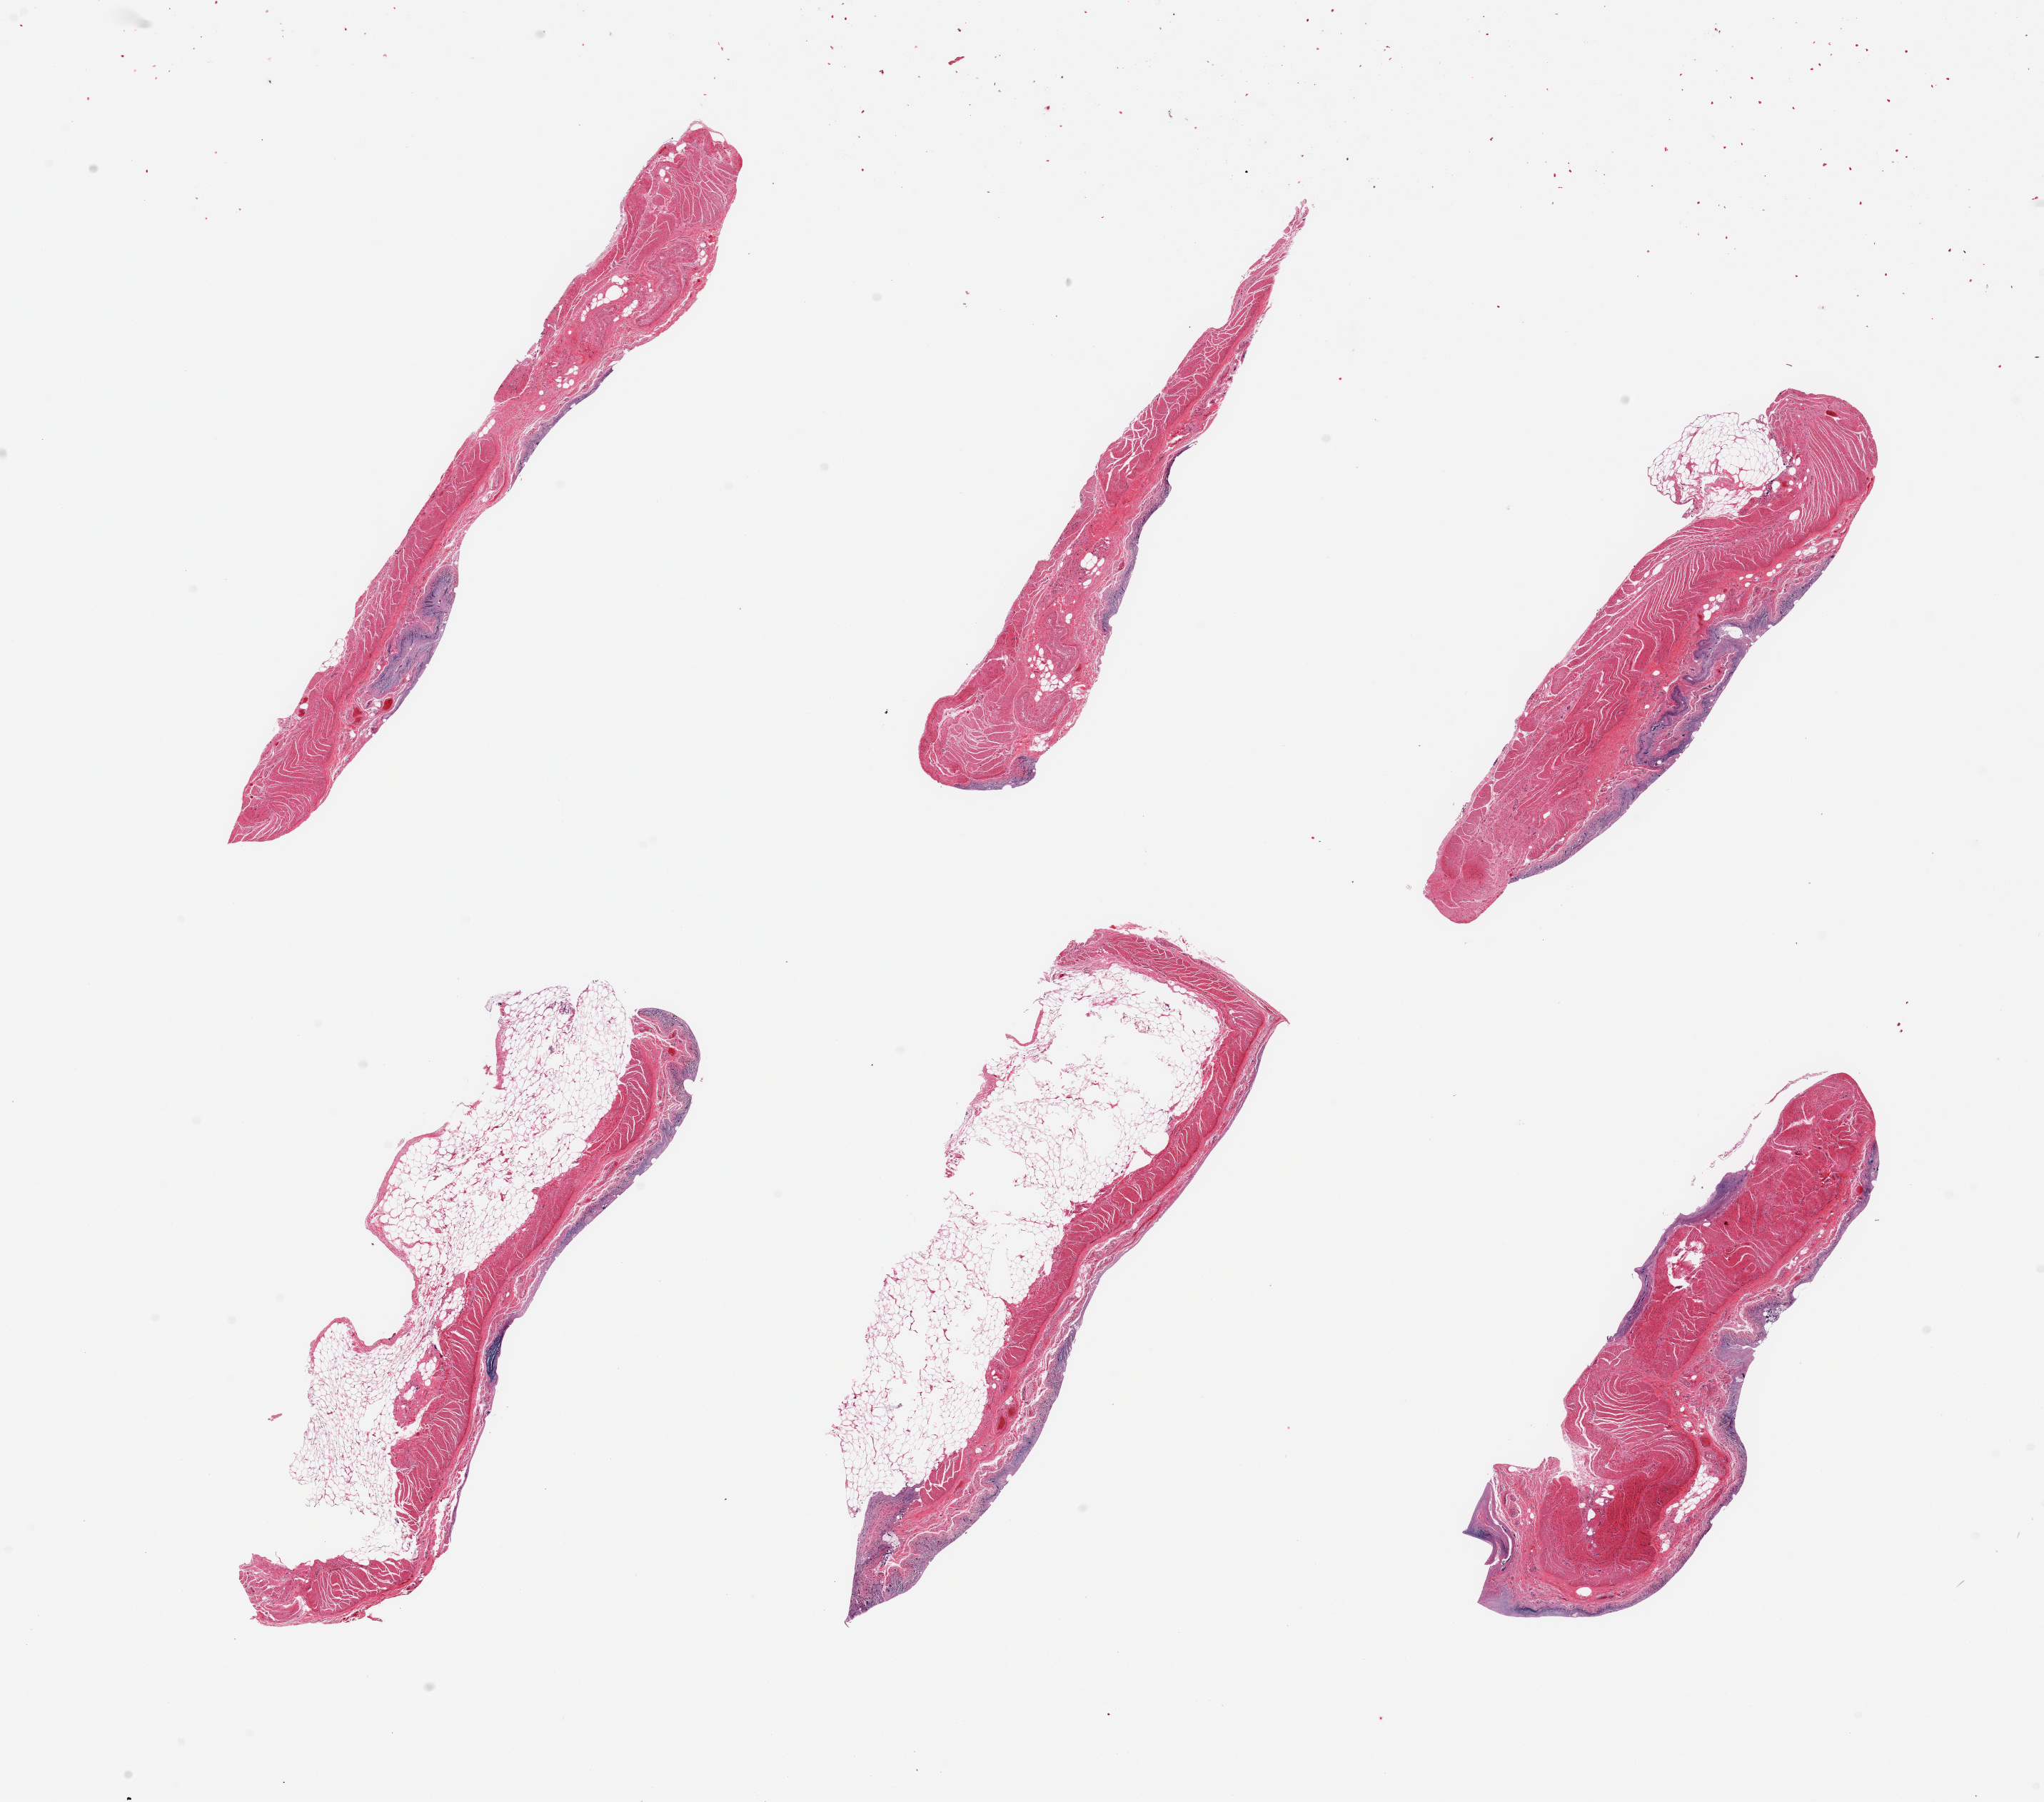
Haematoxylin and eosin whole-slide image — shown as a low-resolution overview of the whole scanned area (about 22.6 x 20.0 mm). PAXgene-fixed, paraffin-embedded tissue. Section of ileum (target tissue). Tissue donor sample.
Pathologist's review note for this sample: 6 pieces; autolyzed mucosa with muscularis and residual fat (not target).